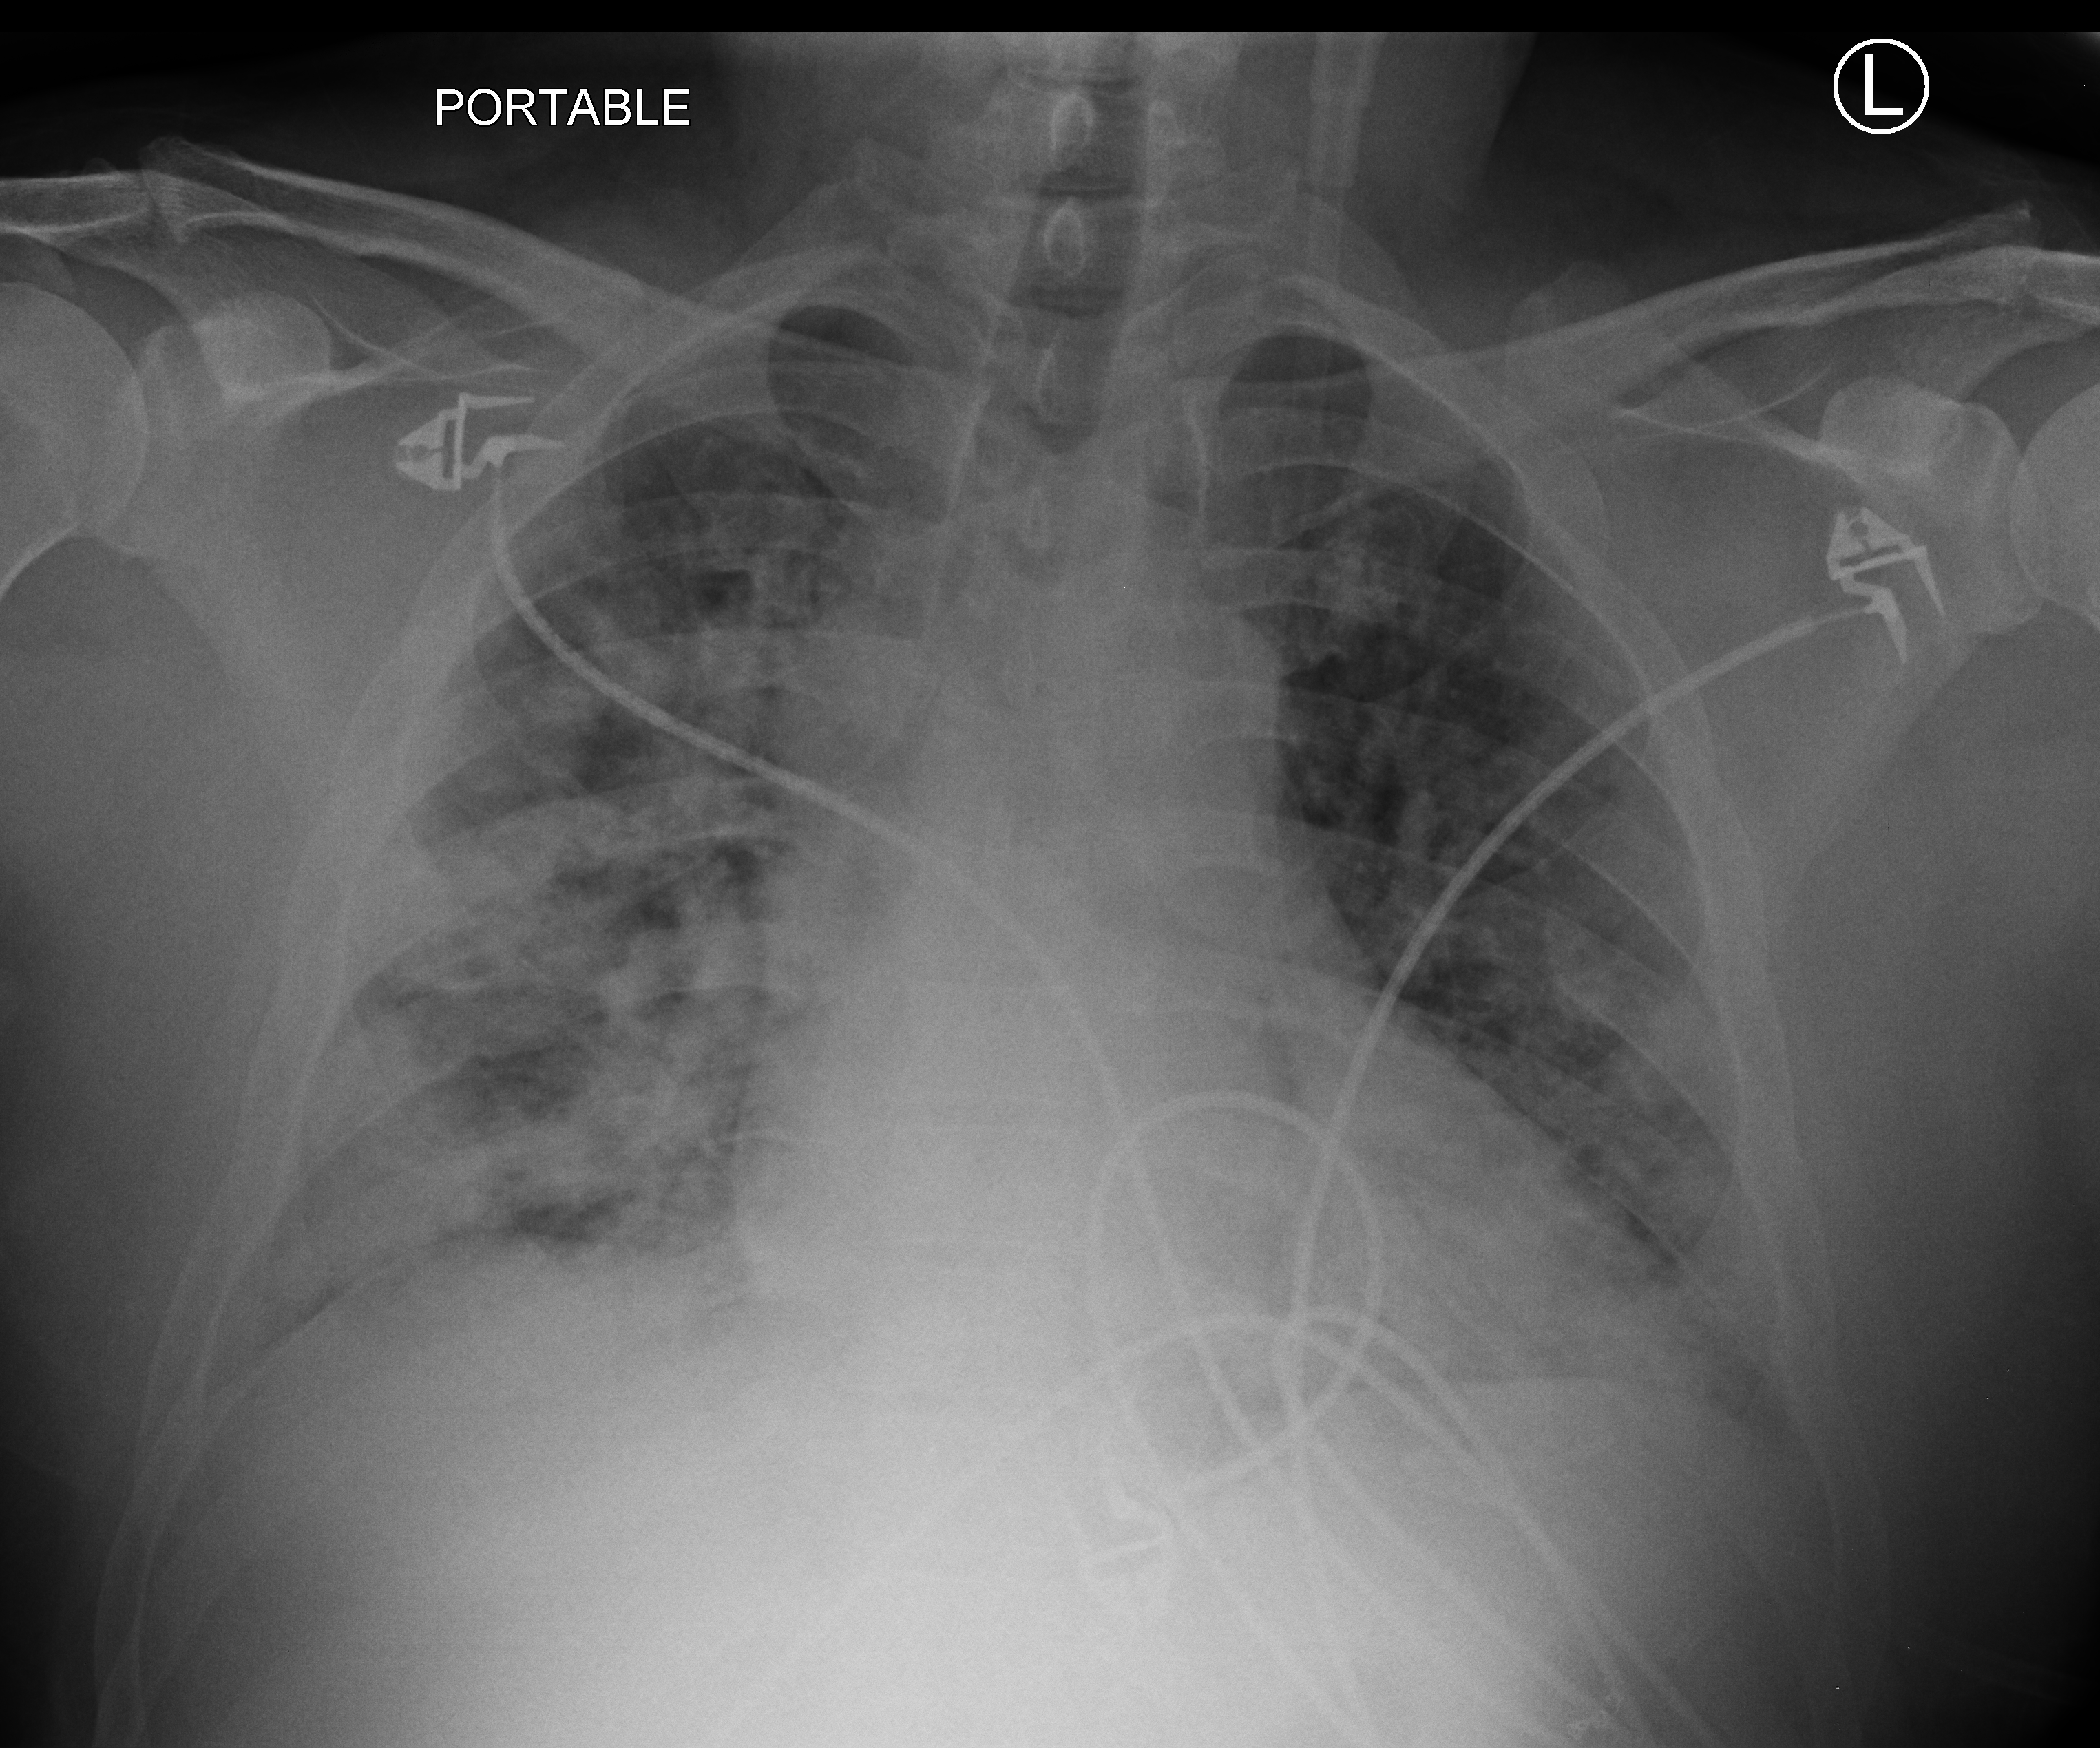
Bedside chest radiograph (computed radiography), anteroposterior (AP) projection. Male patient hospitalised with COVID-19, age 18–59 years.
Hospital-stay facts (about this admission, not read from this image; timing relative to this image not recorded): admitted to intensive care during this hospital stay: no; mechanically ventilated during this hospital stay: no.